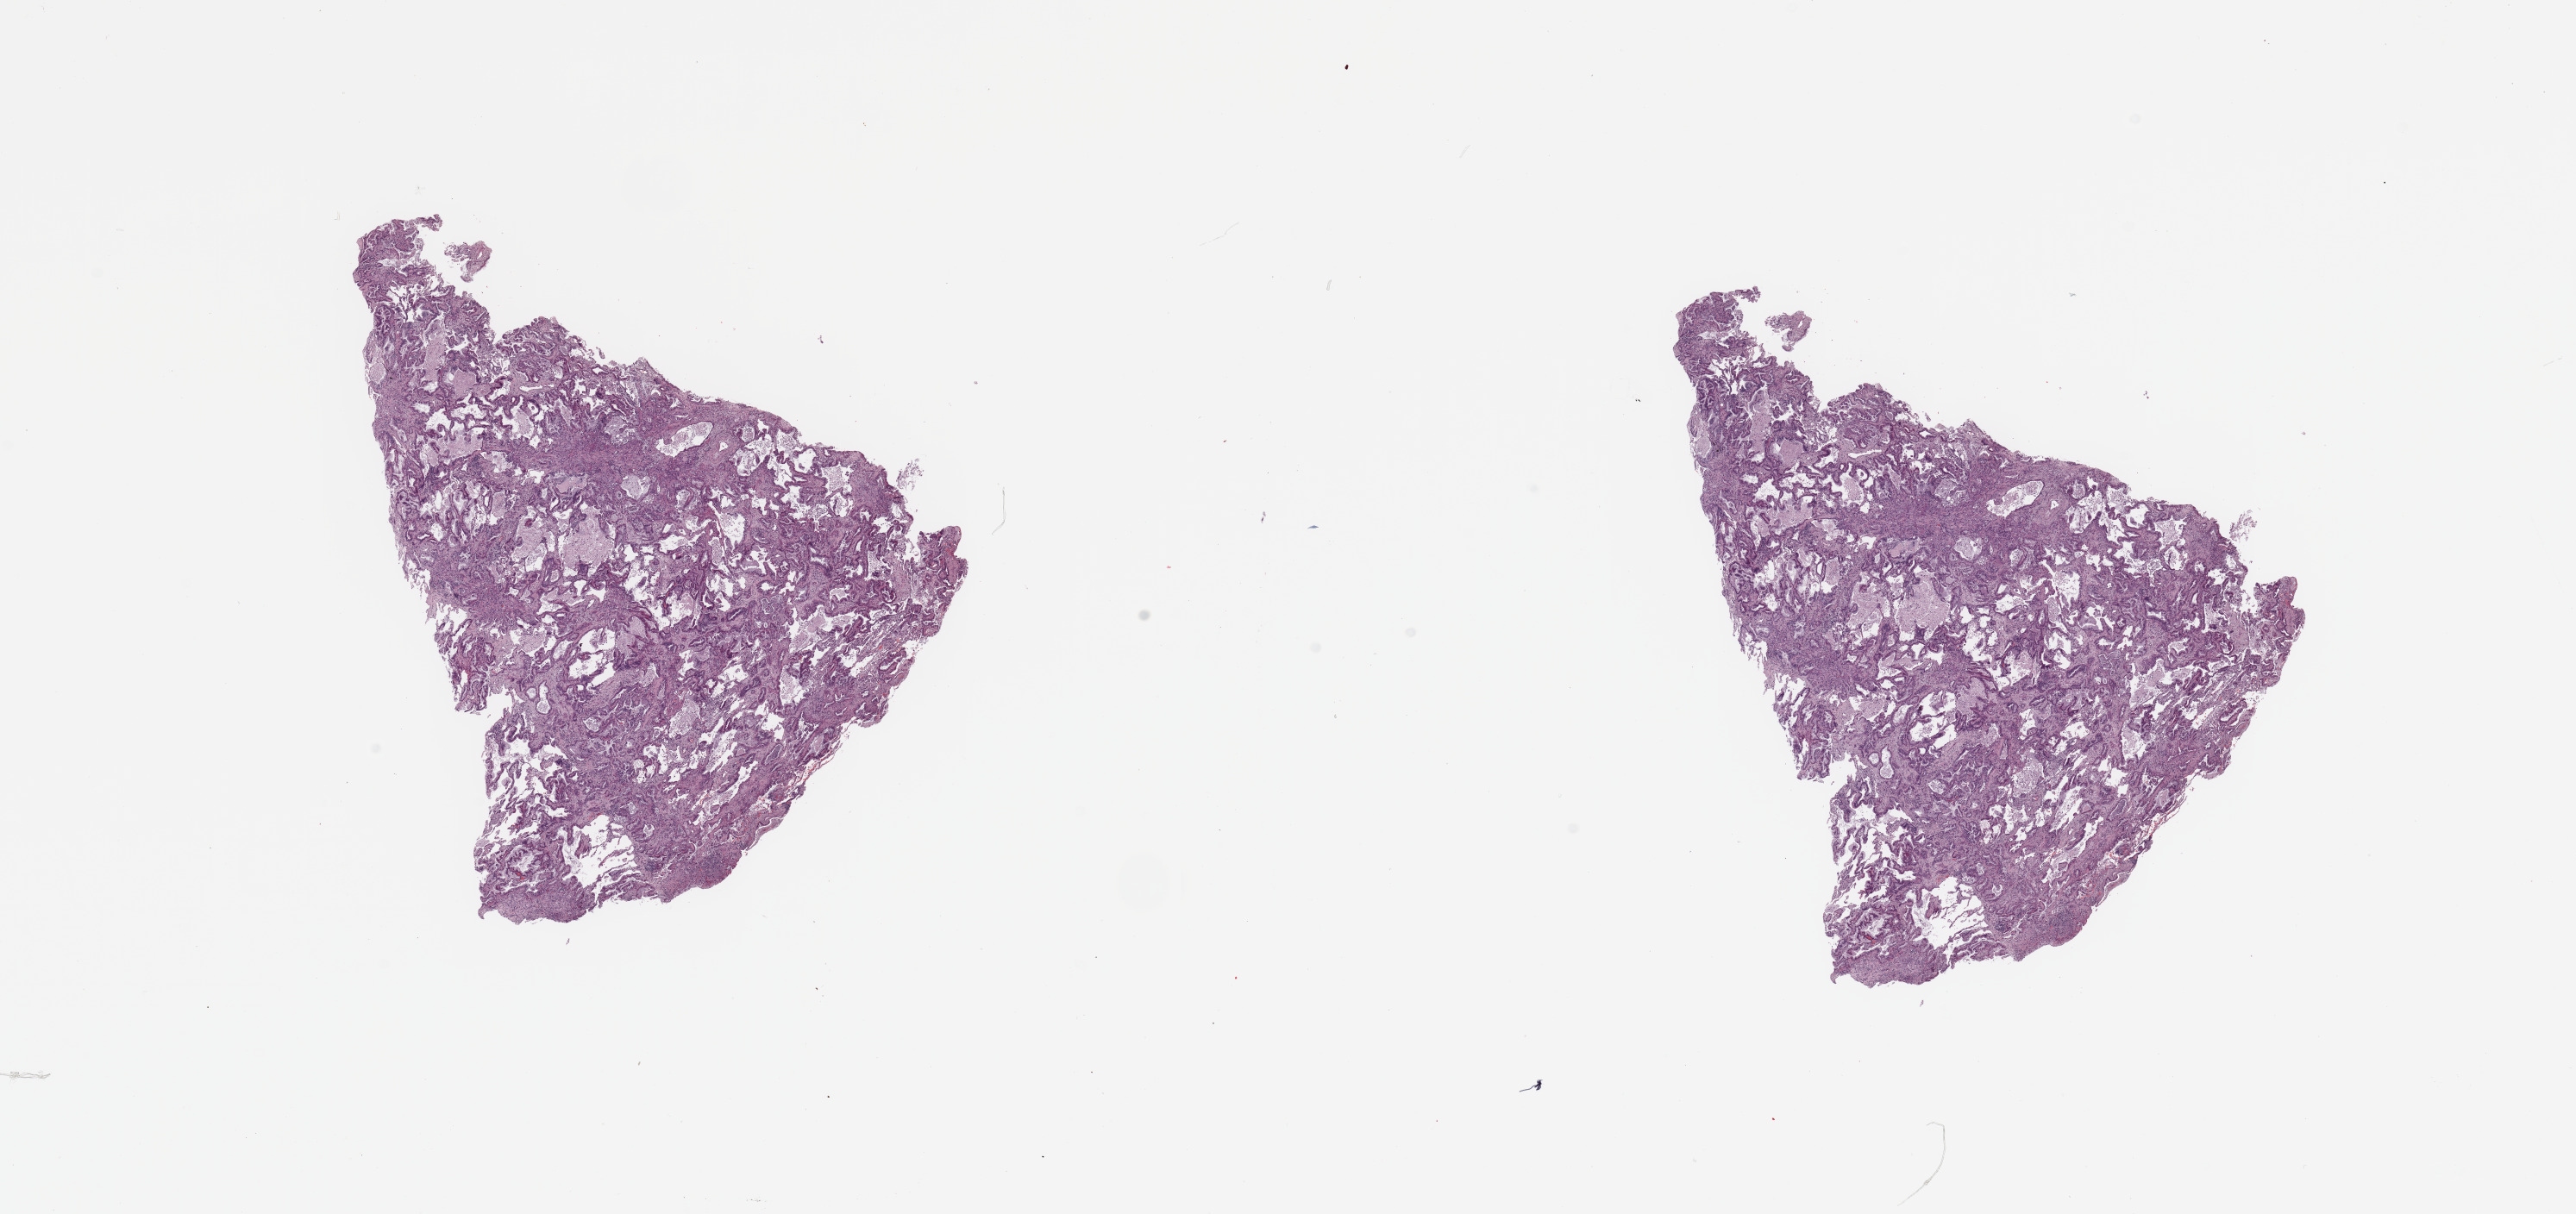
Whole-slide histology image, H&E-stained, shown as a low-resolution overview of the whole scanned area (about 23.6 x 11.1 mm). Lung, tumour tissue. Female, 79 y/o. Histologic grade: G1 (well differentiated).
Diagnosis: Adenocarcinoma, NOS. AJCC pathologic stage: IIB.